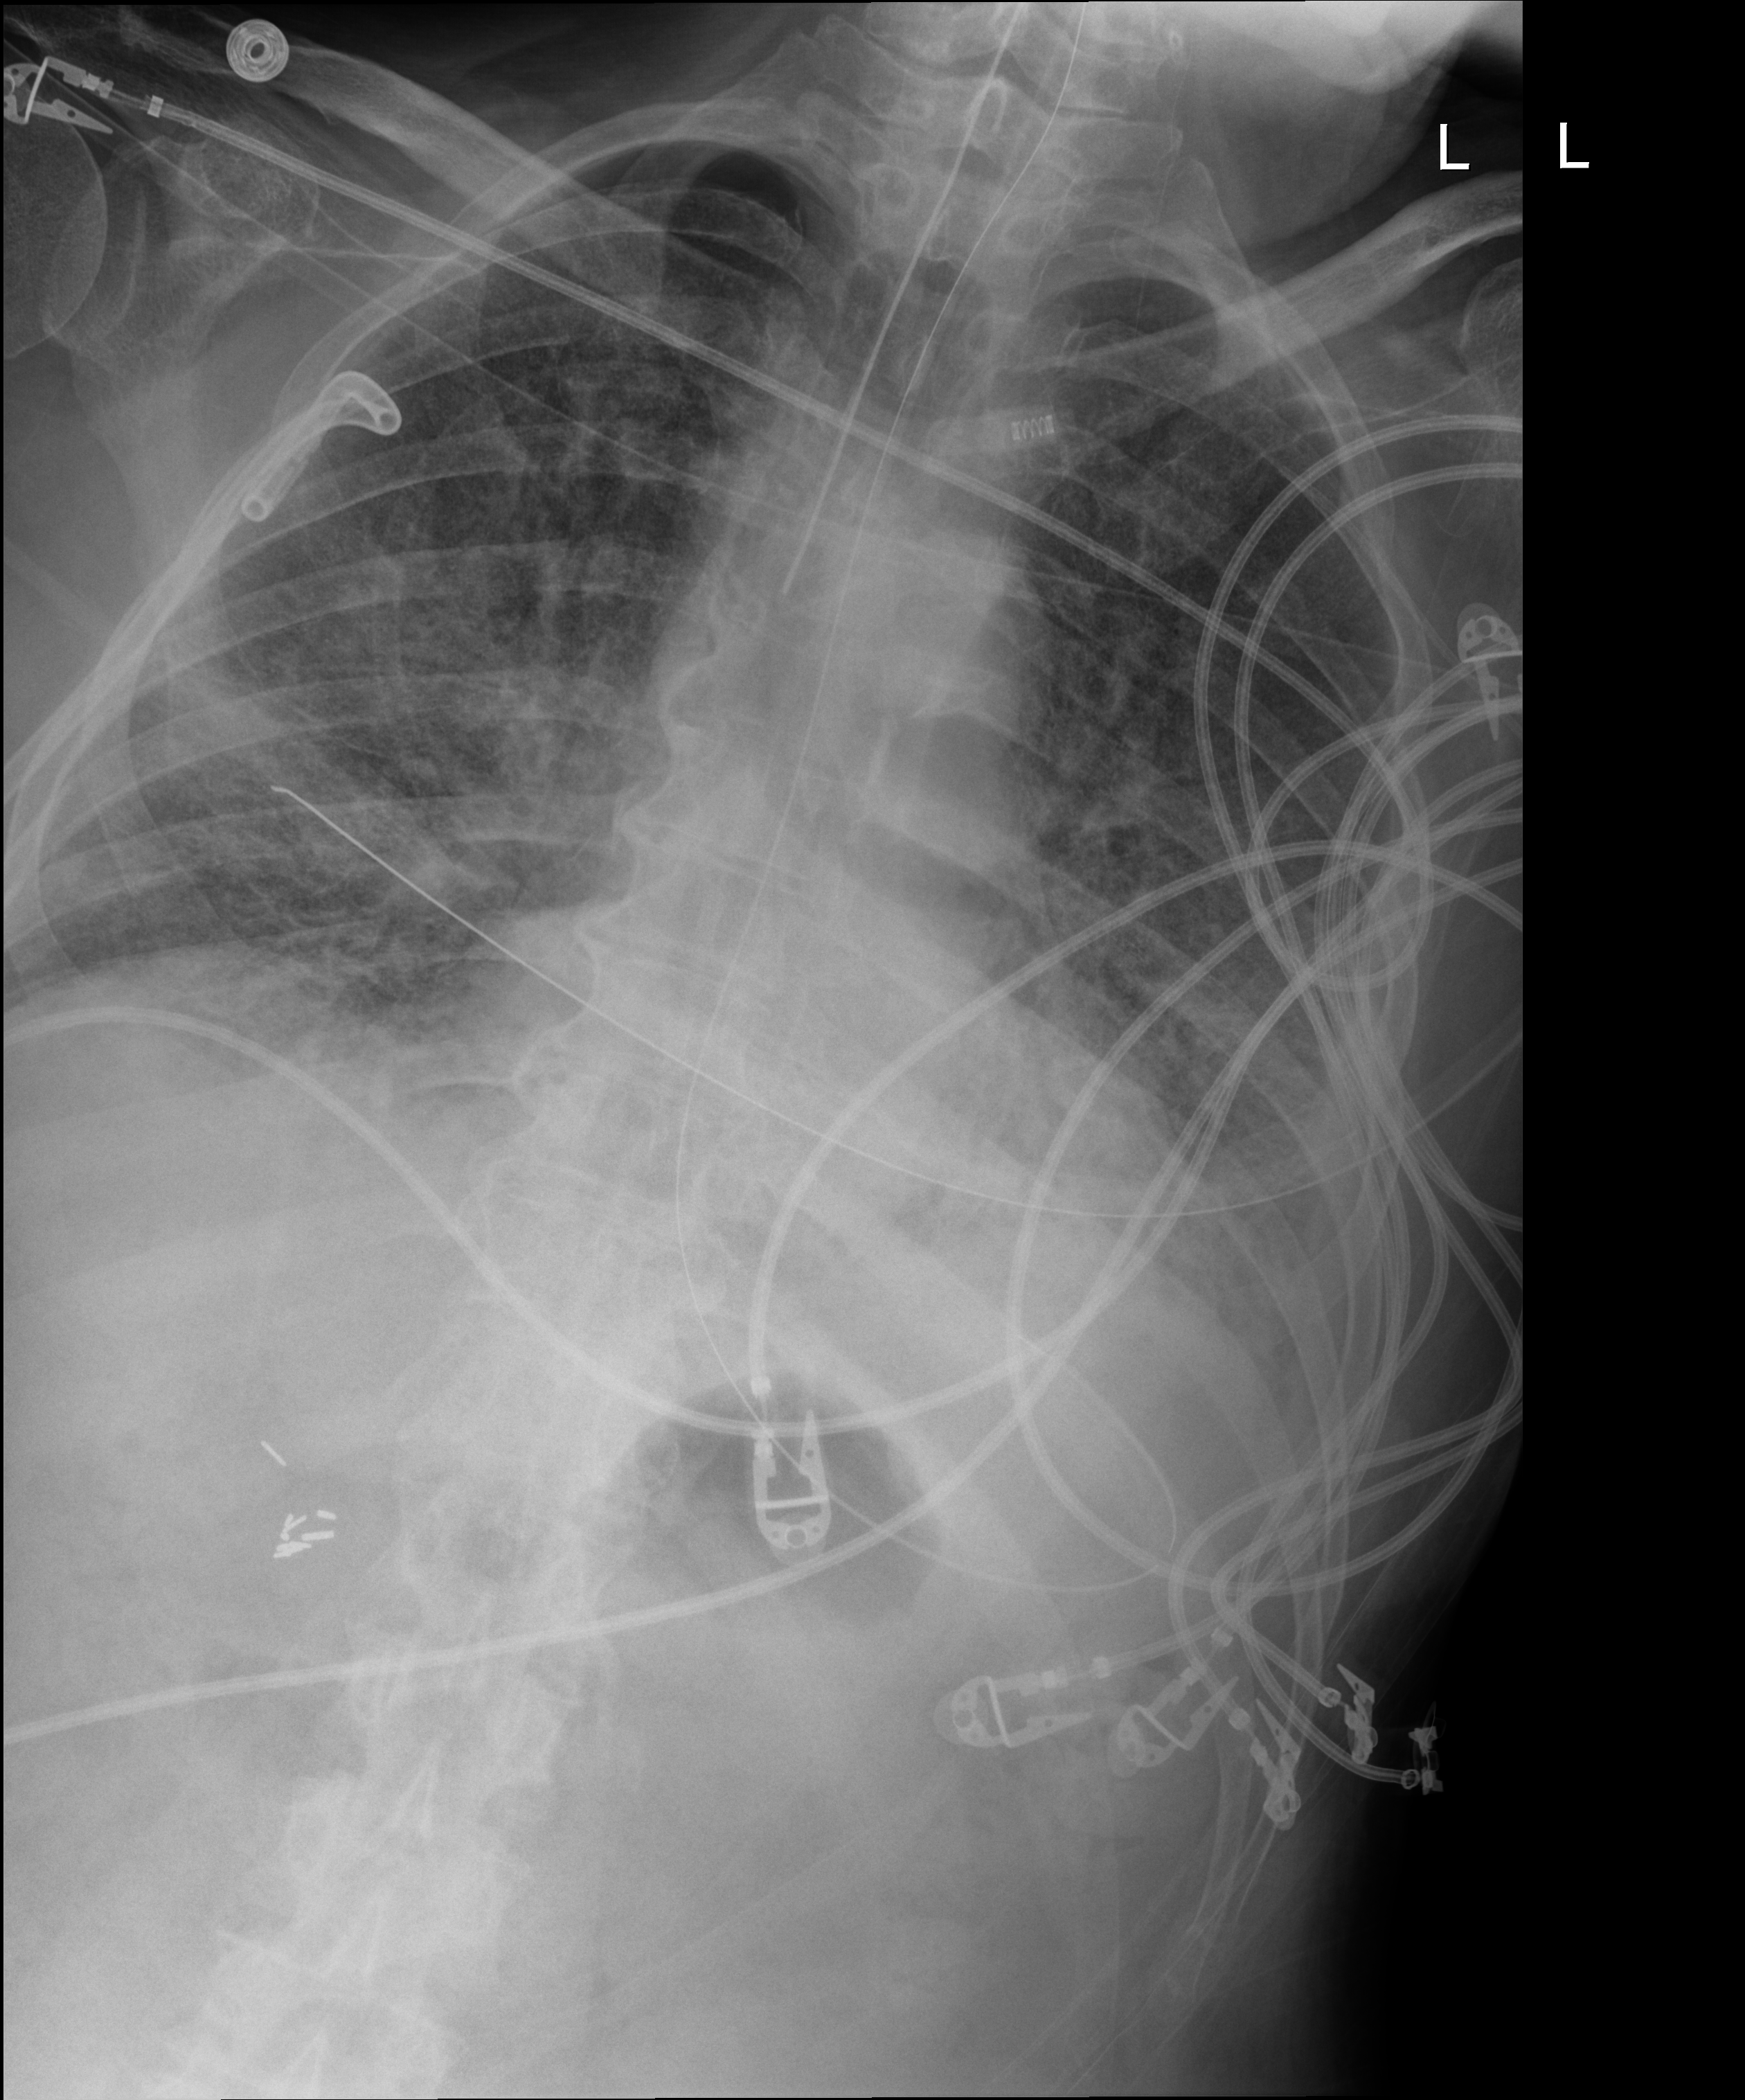
Portable chest radiograph, anteroposterior (AP) projection. Male patient hospitalised with COVID-19, age 75–90 years.
Hospital-stay facts (about this admission, not read from this image; timing relative to this image not recorded): diabetes (admission record): no; mechanically ventilated during this hospital stay: yes; admitted to intensive care during this hospital stay: yes.